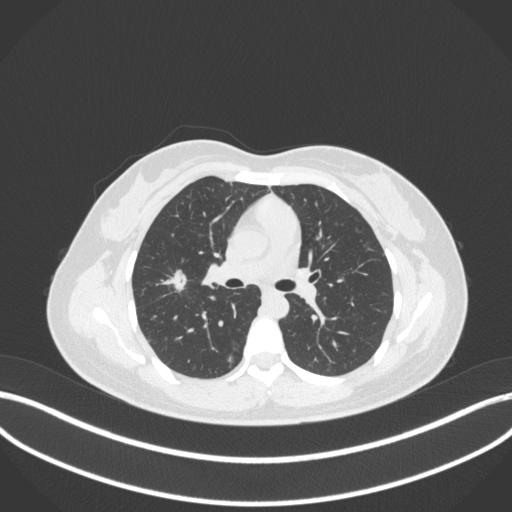
Chest CT, one axial slice. Slice 198 of 214 in the series (ordered by position). Reconstruction kernel B31f. 120 kVp. Lung window (W 1500 / L -600 HU). 1 mm slice thickness. 512 × 512 image matrix, field of view 400 × 400 mm. Female patient, age 33 years. From the clinical record (not read from this slice): clinical TNM (as recorded): T1c N0 M0.
Outlined on this slice (bounding box drawn by a radiologist):
- lung tumour (recorded histology: adenocarcinoma): bounding box (x1, y1, x2, y2) in pixels: (155, 261, 195, 299)